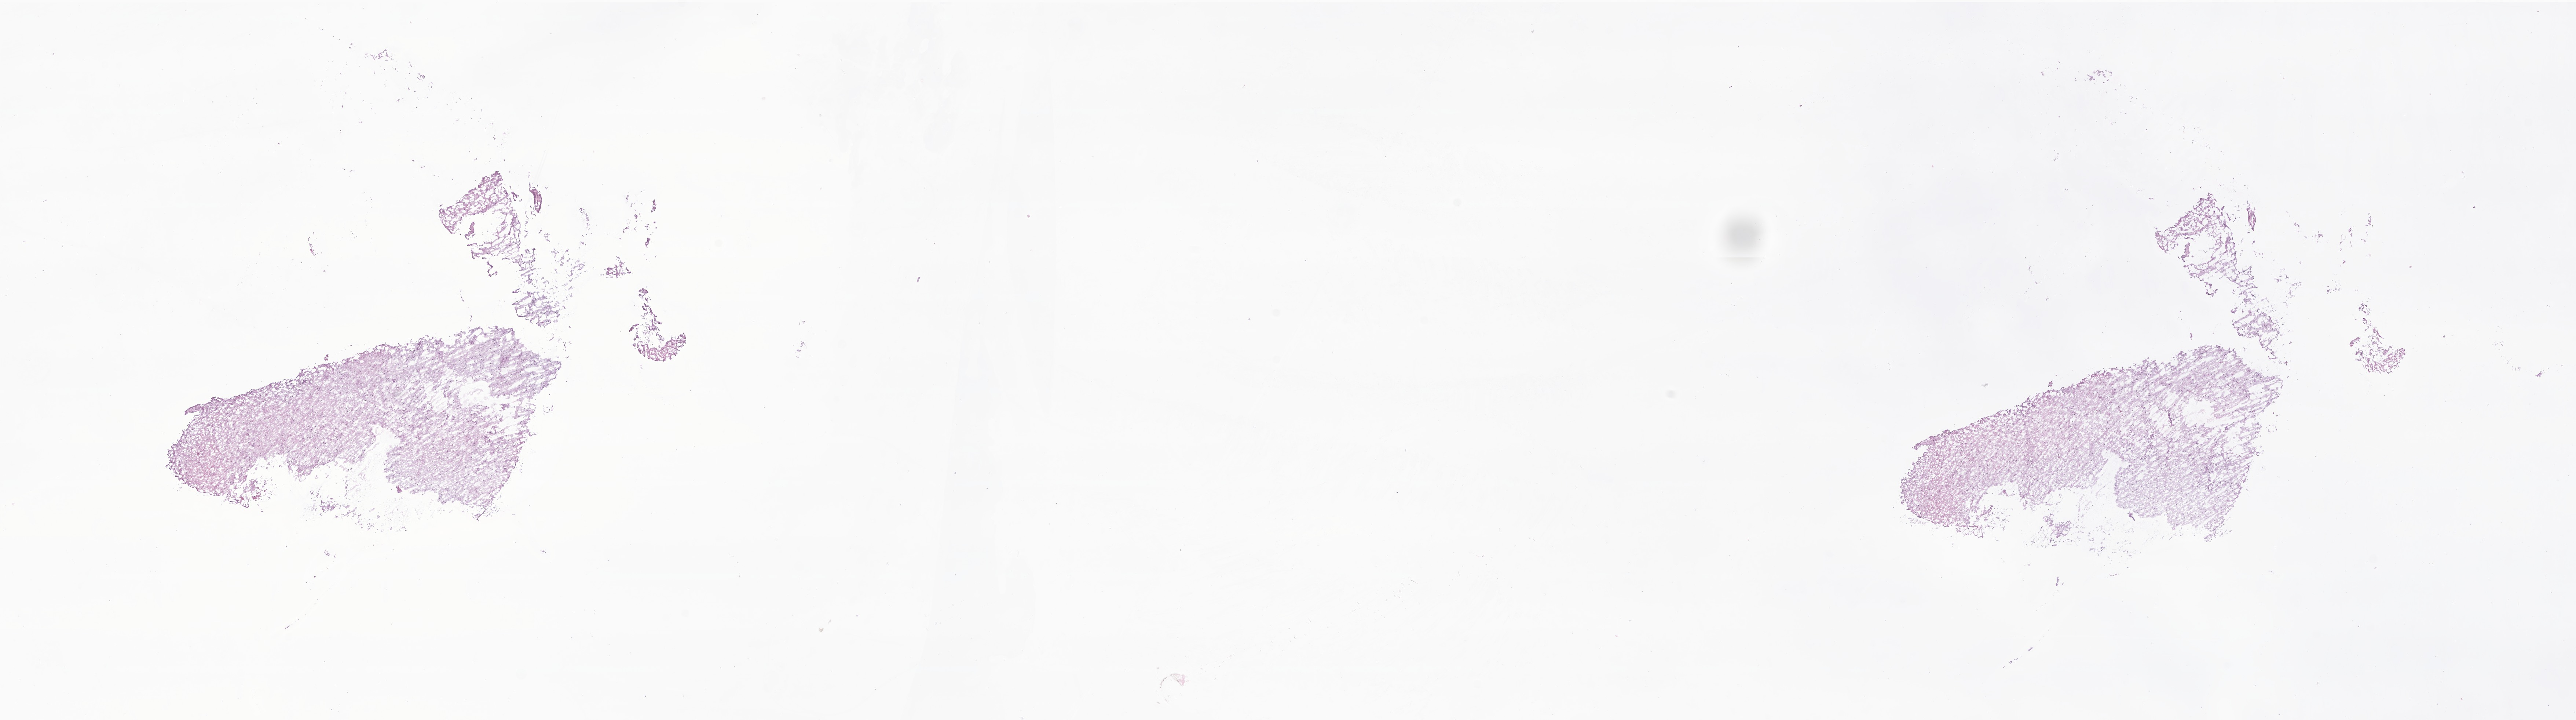
Digitized hematoxylin and eosin (H&E)-stained section of tumor tissue from the cerebellum, a low-resolution overview of the entire scanned area, about 29.6 x 8.3 mm; cryosection (OCT / tissue freezing medium). Patient: female, age 136 months.
Diagnosis (ICD-O-3 morphology term): Pilocytic astrocytoma.